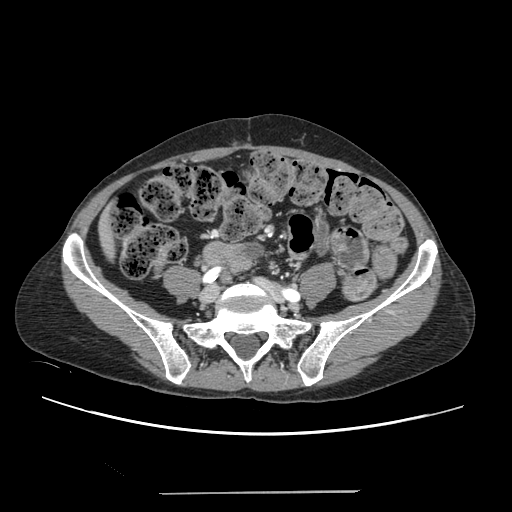
Contrast-enhanced abdominal CT, one axial slice; slice 10 of 240 in the series (ordered by position); 120 kVp; intravenous contrast given; soft-tissue window (W 400 / L 40 HU); 512 × 512 image matrix, field of view 371 × 371 mm. Female patient, age 60 years. From the clinical record (not read from this slice): diagnosis: colorectal cancer liver metastases, imaged before liver resection; multiple liver metastases: no; largest metastasis: 1.5 cm; chemotherapy before resection: yes.
Outlined on this slice (expert manual segmentation):
- liver: bounding box (x1, y1, x2, y2) in pixels: (101, 222, 112, 252)
- planned liver remnant (the part of the liver to remain after resection): (101, 220, 112, 252)